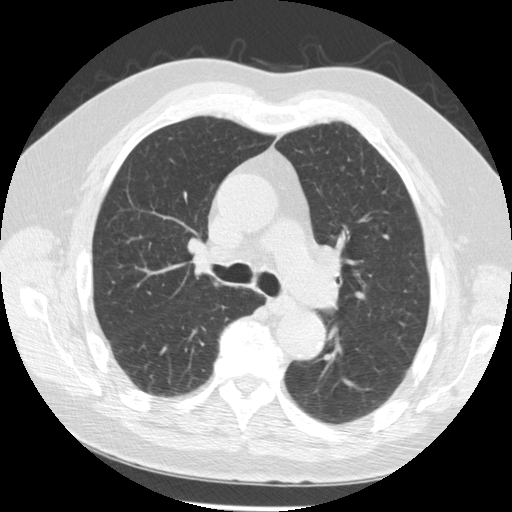
Low-dose screening chest CT, one axial slice; slice 167 of 259 in the series (ordered by position); reconstruction kernel STANDARD; lung window (W 1500 / L -600 HU); 2.5 mm slice thickness; 512 × 512 image matrix, field of view 355 × 355 mm.
Structures marked on this image (outlined manually by an expert reader):
- lesion 2 (tumor, hilum of right lung): bounding box (x1, y1, x2, y2) in pixels: (193, 251, 209, 272)